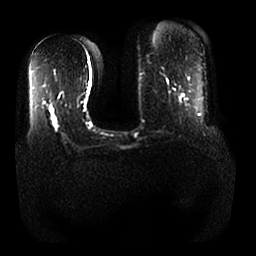
Breast MRI, one axial slice; slice 12 of 25 in the series (ordered by position); diffusion-weighted series; image 2 of 4 stored at this slice position (different b-values; order by instance number); 1.5 T; 256 × 256 image matrix. Female patient.
Annotated regions visible in this slice (outlined manually by an expert reader):
- tumour on diffusion-weighted imaging: box from (x=54, y=117) to (x=57, y=131) px